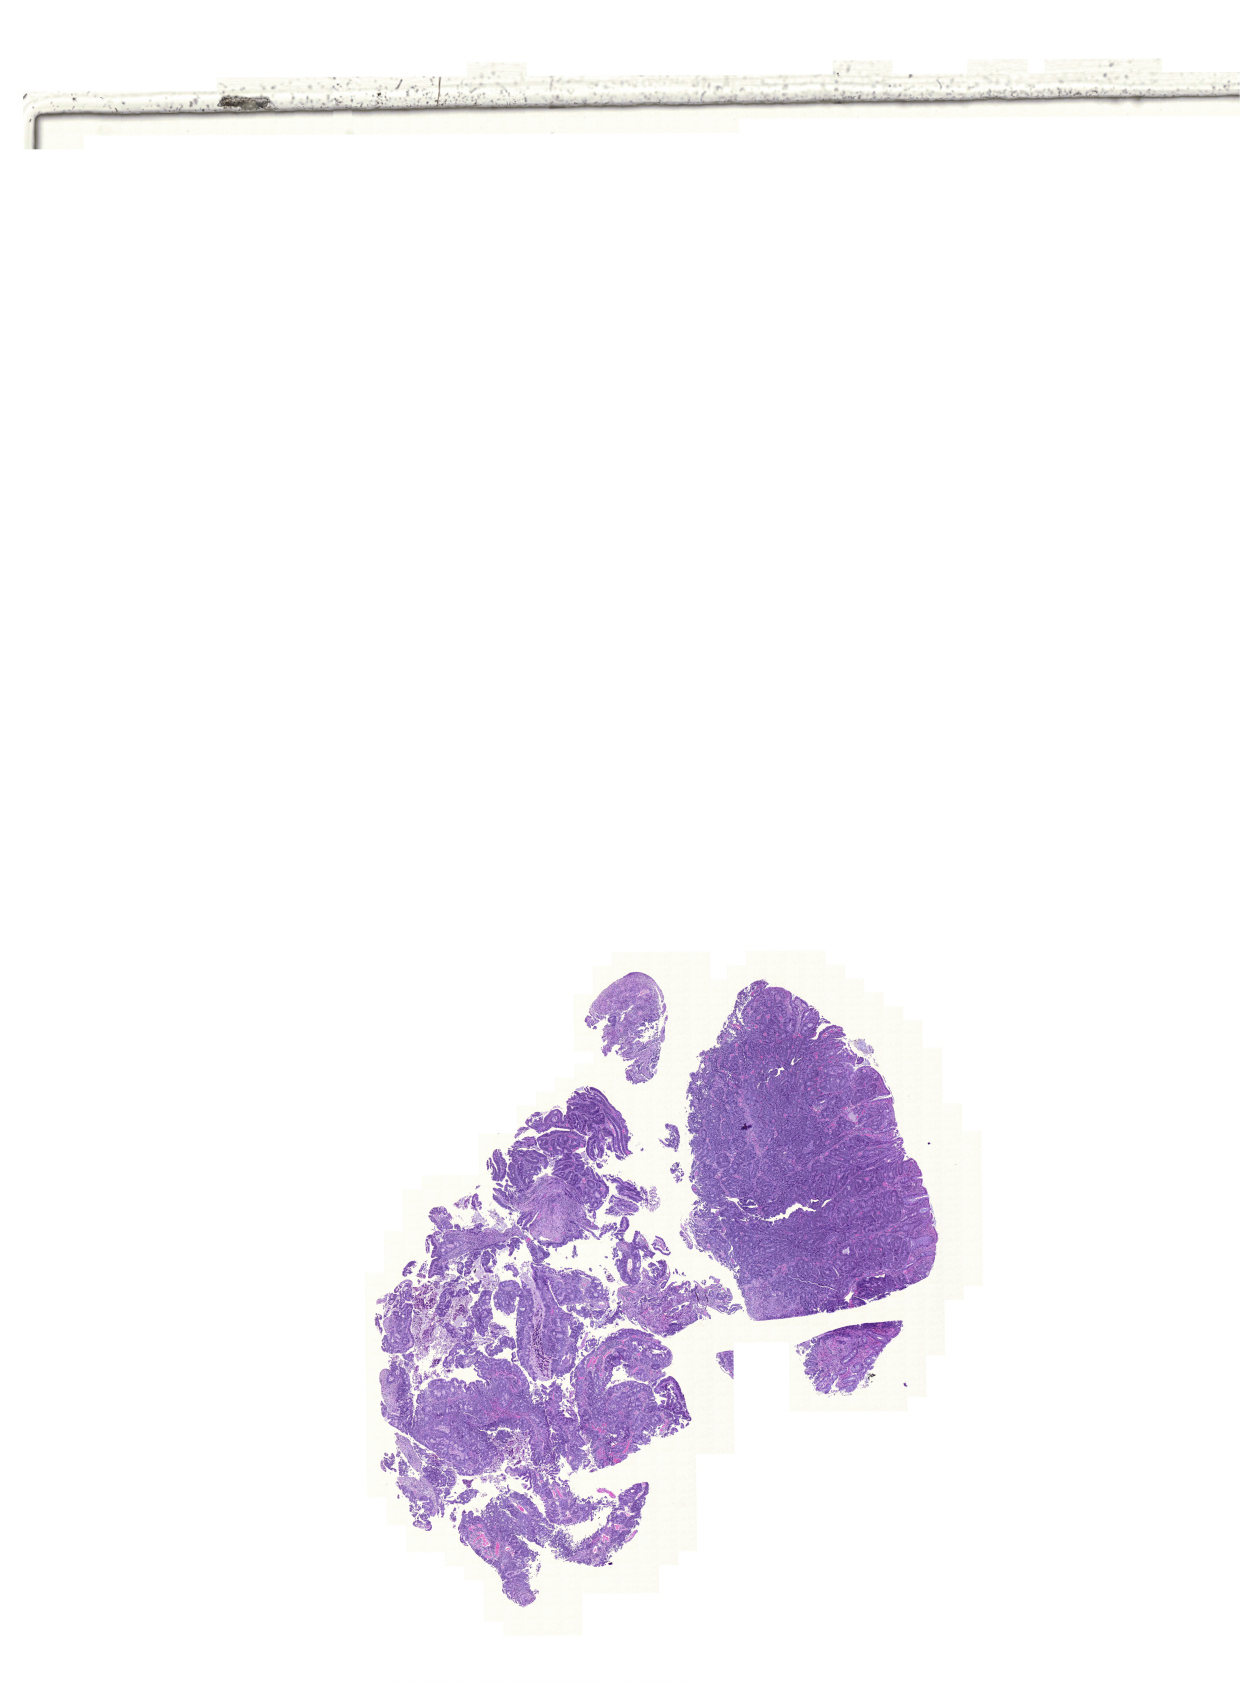
Digitized Hematoxylin and eosin (H&E) stained tissue section (whole slide) — a low-resolution overview of the entire scanned area, about 18.5 x 25.1 mm (slide scanned at 20x); formalin-fixed paraffin-embedded (FFPE) diagnostic section; rectum, primary tumour sample. Patient: female, age at initial diagnosis 49 years.
* lymph nodes positive (case pathology): 1 of 24 examined
* AJCC pathologic stage: IIIB
* pathologic diagnosis: Adenocarcinoma, NOS
* TNM: T3 N1 M0